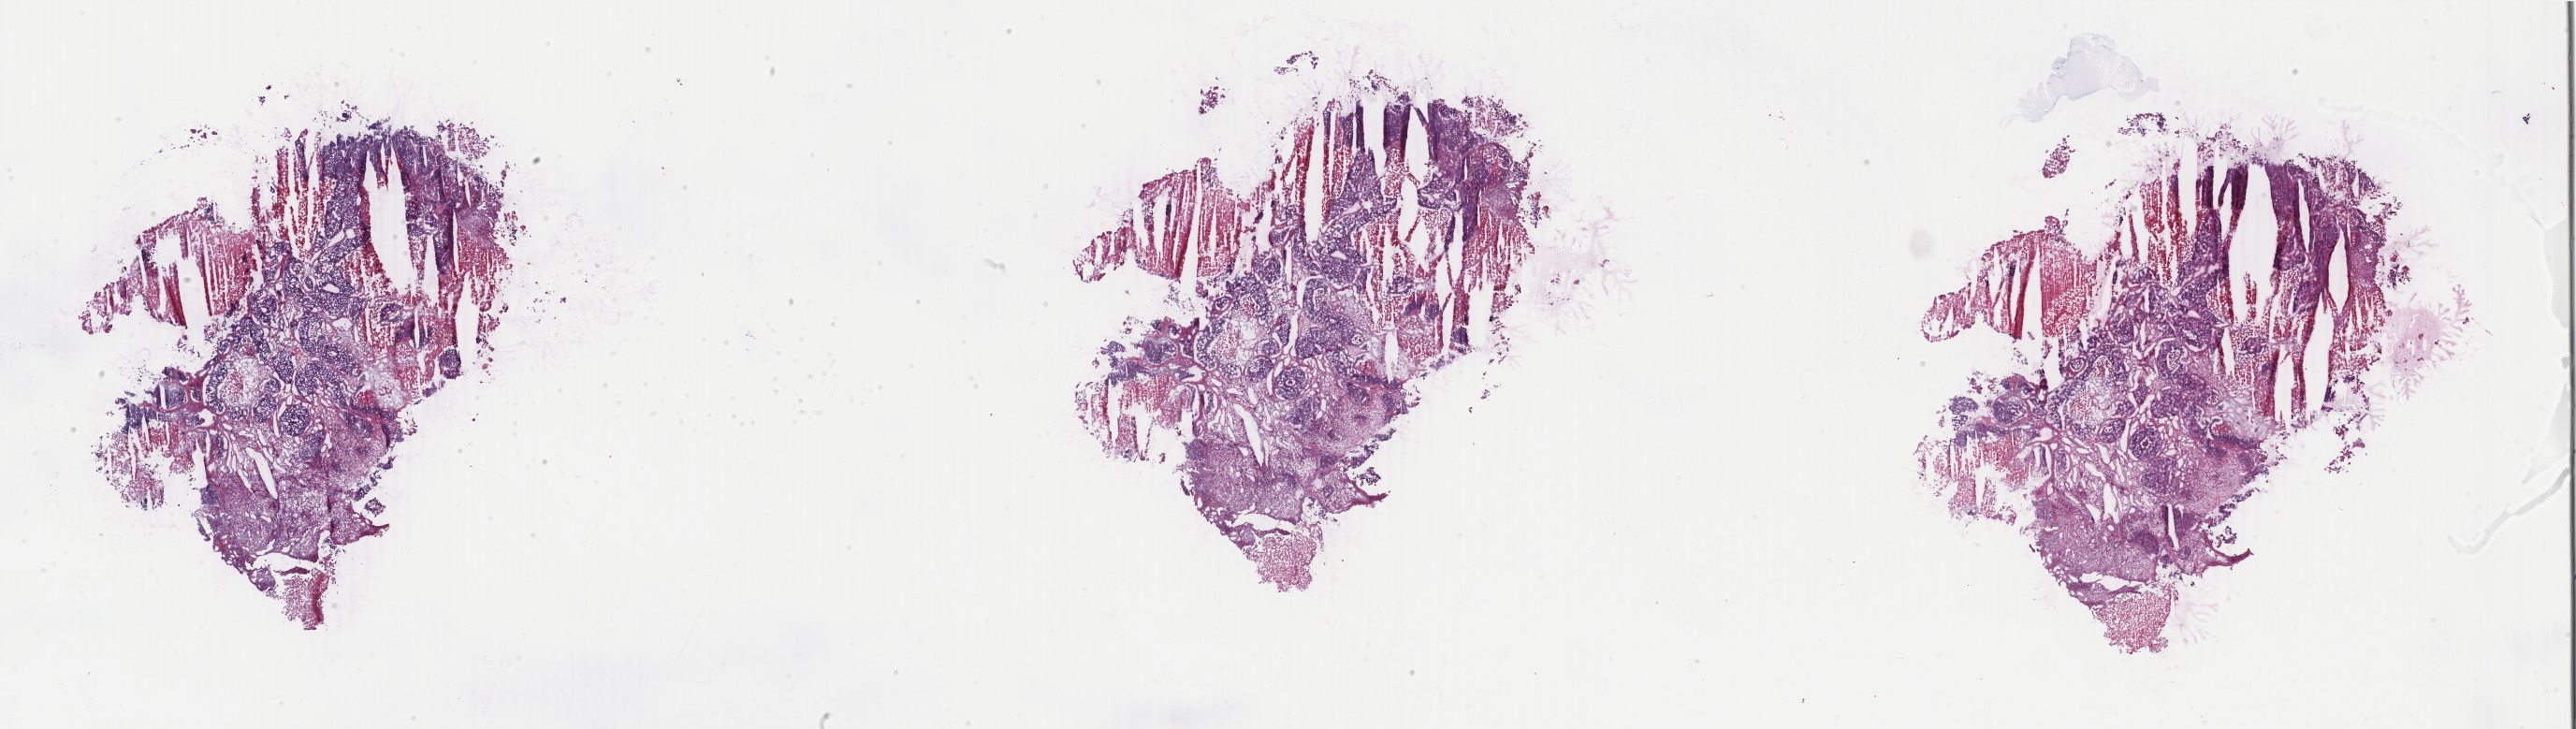
Digitized Hematoxylin and eosin (H&E) stained tissue section (whole slide) — shown as a low-resolution overview of the whole scanned area (about 43.8 x 12.4 mm, acquisition: 40x scan). Frozen section from the top of the tissue portion. Primary tumour sample from the breast. Female, age 73 years at initial diagnosis. Pathologist review of this section (percent, as recorded): tumour cells 65%, tumour nuclei 65%, normal cells 0%, stromal cells 5%, necrosis 30%. Inflammatory infiltration, as recorded: lymphocyte infiltration 0%, monocyte infiltration 0%, neutrophil infiltration 0%.
TNM: T2 N0 M0. Lymph nodes positive (case pathology): 0 of 7 examined. Laterality: left. AJCC pathologic stage: IIA. Pathologic diagnosis: Infiltrating duct carcinoma, NOS.